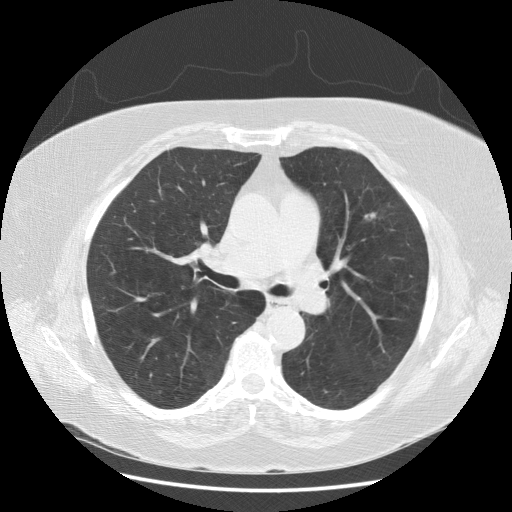
Low-dose screening chest CT, axial slice; second screening round (one year after baseline); lung window (W 1500 / L -600 HU); slice 67 of 164 in the series. Female participant, aged 68 years at enrolment. Current smoker at enrolment.
Expert reader's lesion annotation, bounding box [x1, y1, x2, y2] px = [359, 195, 400, 236]. The screening reader recorded 2 non-calcified nodules or masses ≥4 mm on this exam (left upper lobe, right upper lobe); which of them this box marks is not recorded. Lung cancer was diagnosed 90 days after this screen: large cell carcinoma, NOS, left upper lobe, undifferentiated (G4), stage IA (AJCC 6th edition), 10 mm at pathology.